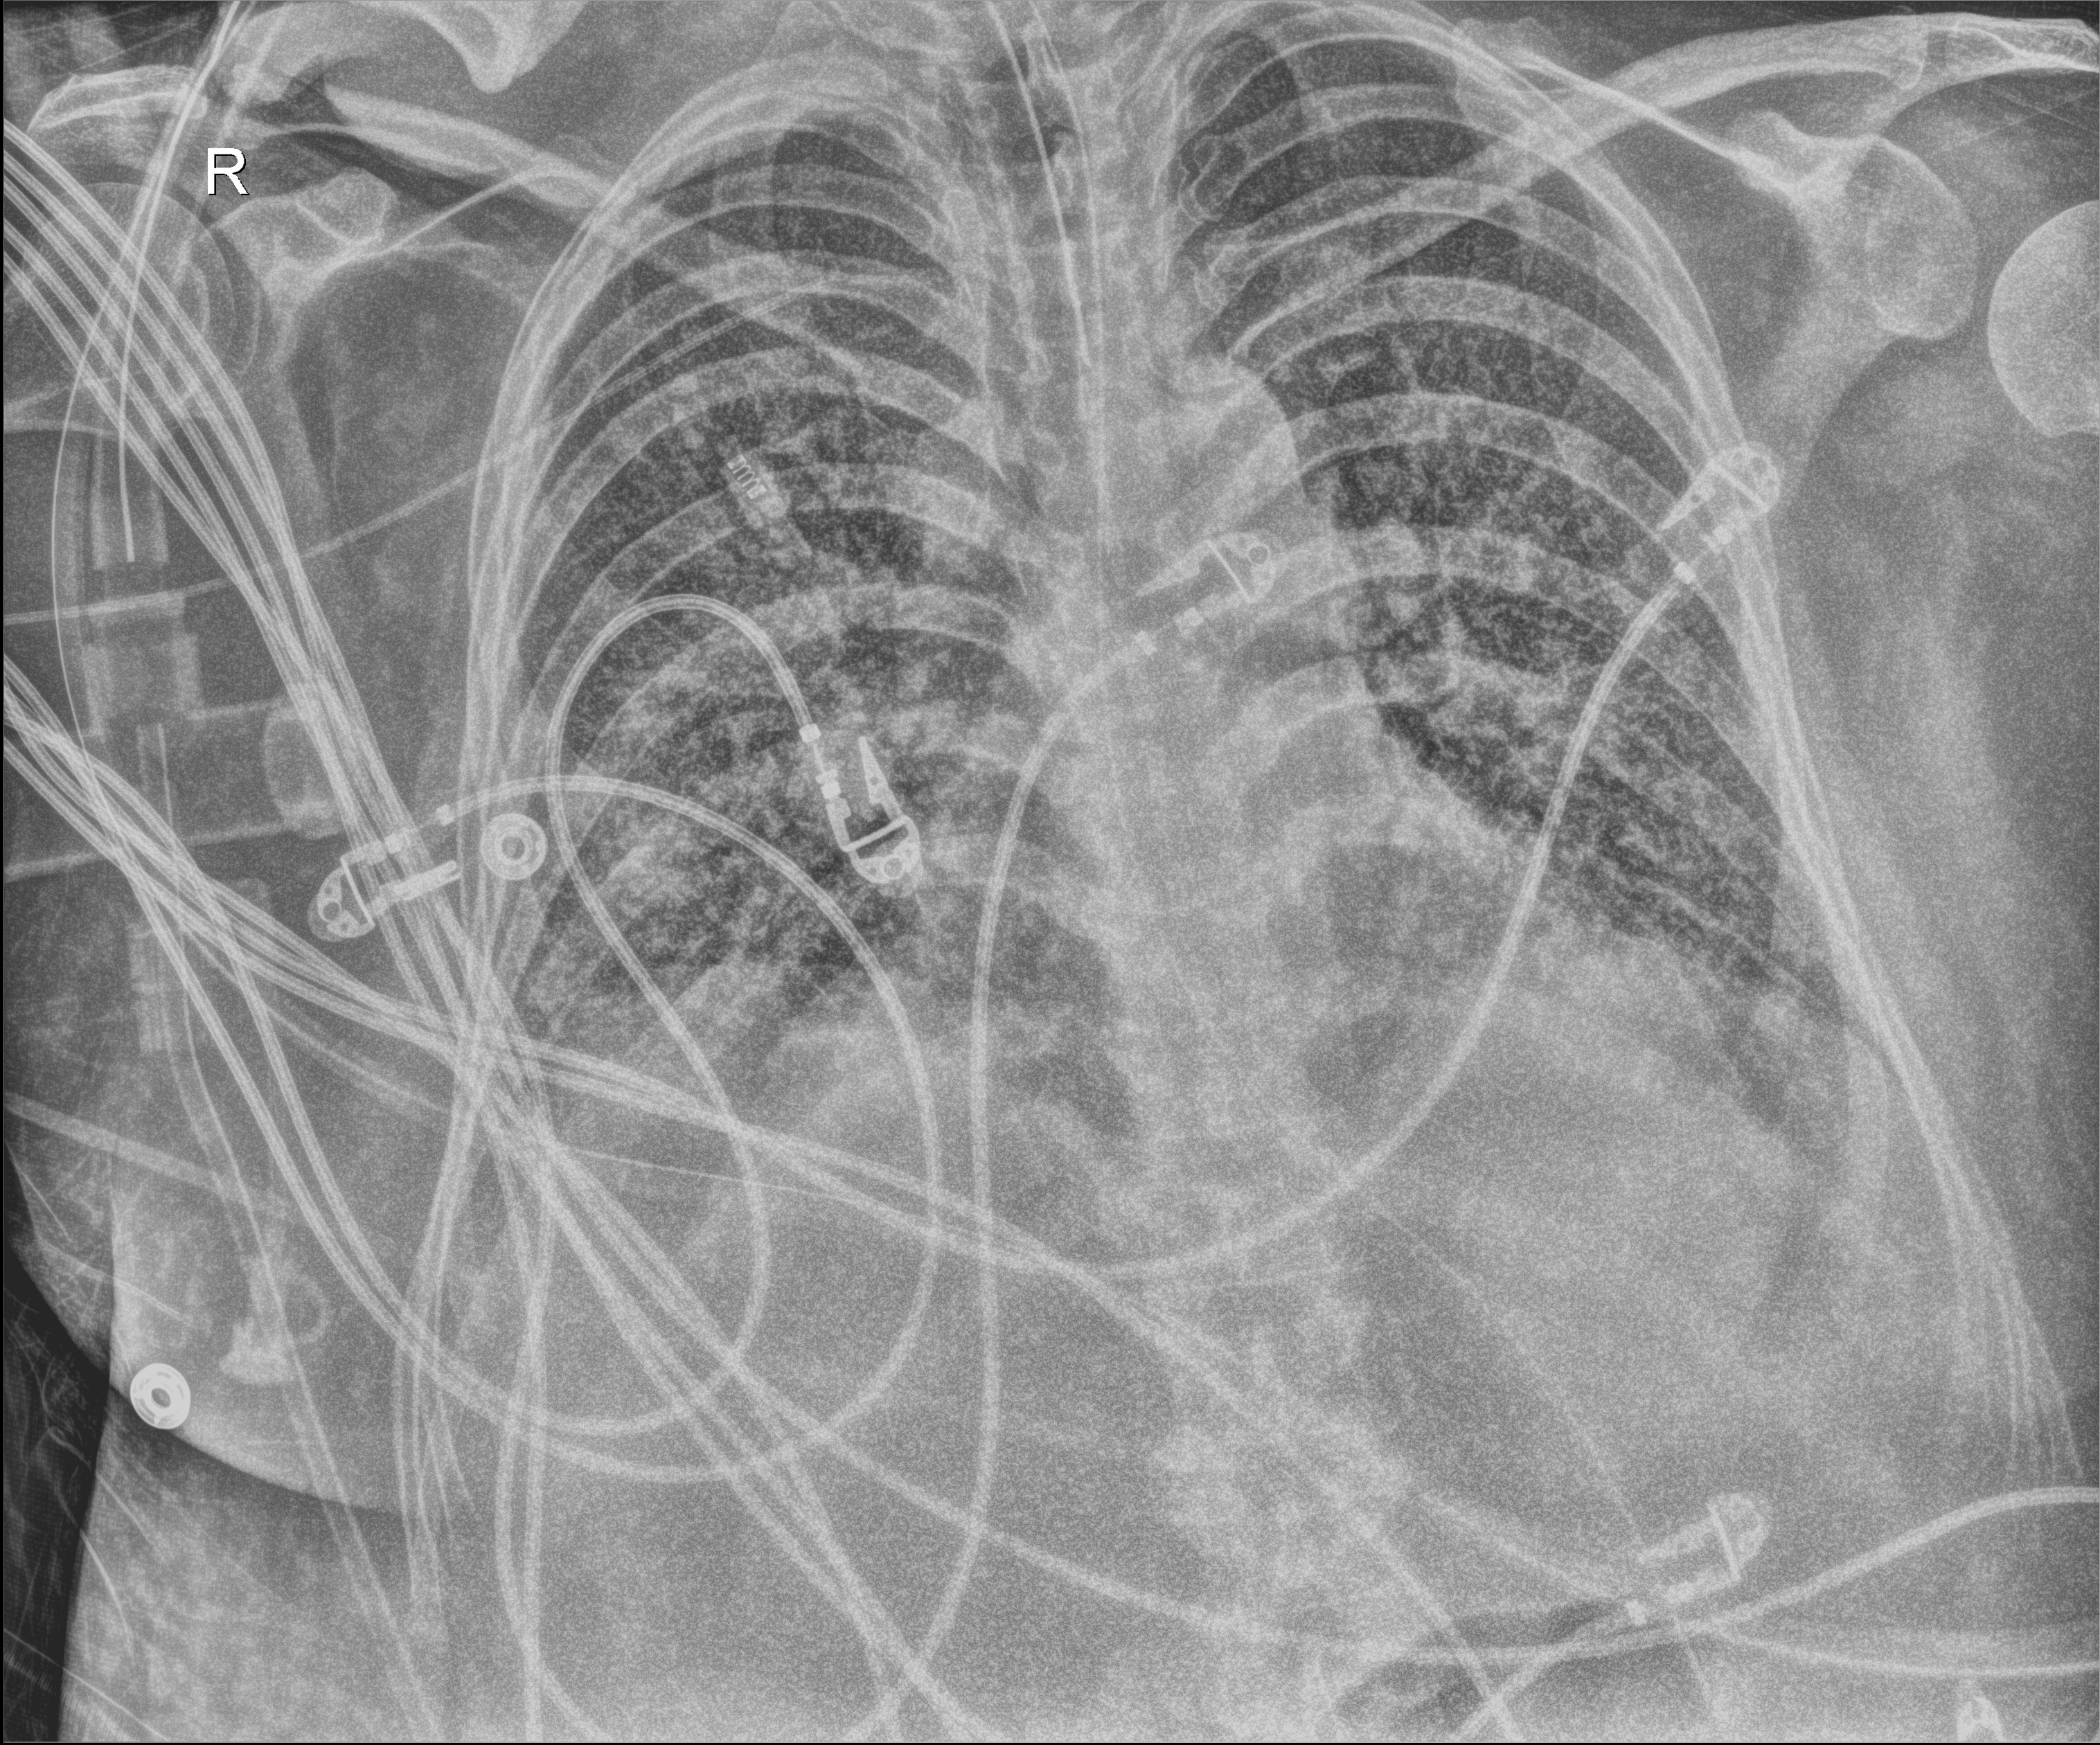
Bedside chest radiograph (digital radiography). Patient hospitalised with COVID-19, aged 18–59 years.
Hospital-stay facts (about this admission, not read from this image; timing relative to this image not recorded): admitted to intensive care during this hospital stay: yes.